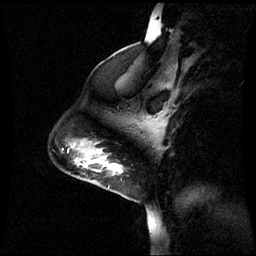
Breast MRI (dynamic contrast-enhanced), one sagittal slice; slice 15 of 60 in the series (ordered by position); dynamic contrast-enhanced series, image 2 of 3 at this slice position (ordered by acquisition); 1.5 T; TE 4.2 ms, TR 8.9 ms; 2.2 mm slice thickness; 256 × 256 image matrix. Female patient, age 44 years. From the clinical record (not read from this slice): setting: breast cancer imaged before/during neoadjuvant chemotherapy; receptor status: triple-negative.
Structures marked on this image (semi-automatic segmentation, software-assisted and operator-edited):
- analysis volume of interest (the breast-tissue region the enhancement analysis was run in; not a lesion): bounding box <76,150,123,185> (left, top, right, bottom; pixels)
- tumour enhancement mask (voxels above the 70 % enhancement threshold inside the analysis volume of interest): <86,160,122,173>